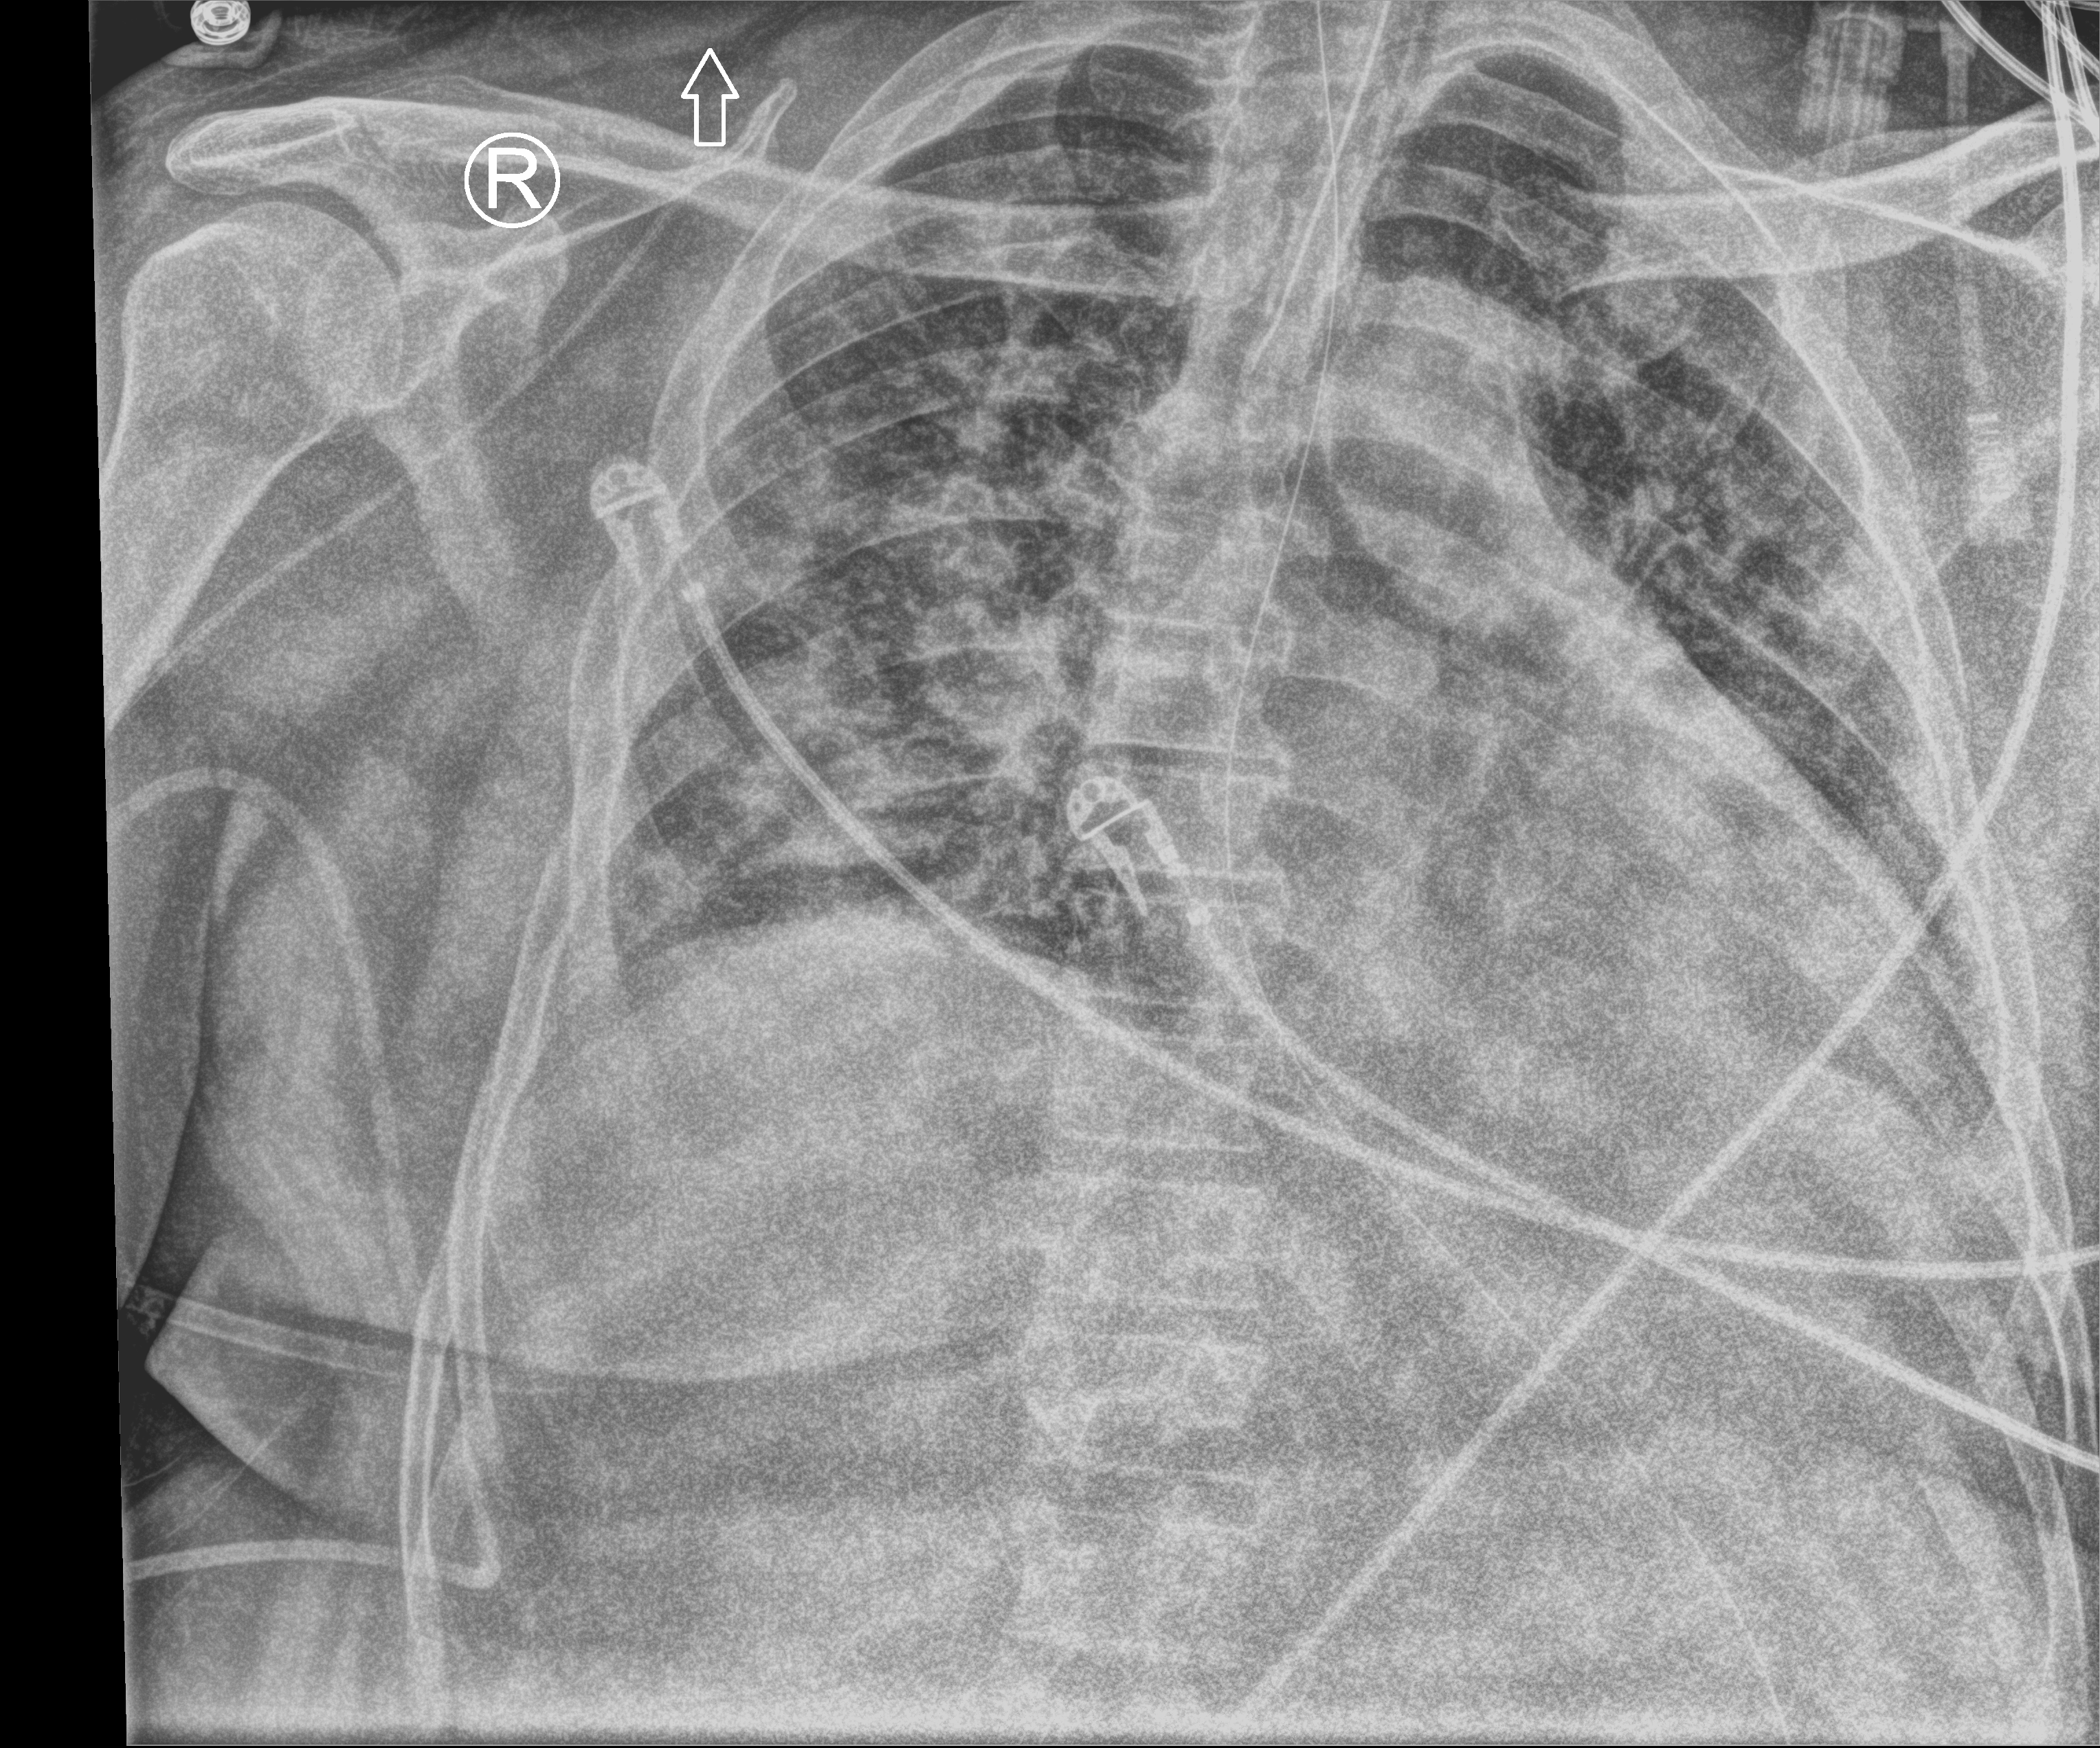
Portable chest radiograph. Male patient hospitalised with COVID-19, age 18–59 years.
From the hospital-stay record, not from the radiograph (when in the stay this image was taken is not recorded):
- diabetes (admission record): no